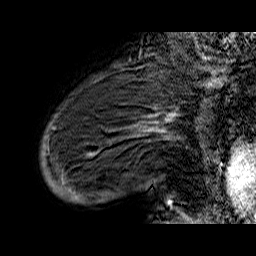
Breast MRI (dynamic contrast-enhanced), one sagittal slice. Slice 9 of 60 in the series (ordered by position). Dynamic contrast-enhanced series, time point 2 of 6 at this slice position (early post-contrast). 1.5 T. TE 6.5 ms, TR 32.9 ms. 4 mm slice thickness. 256 × 256 image matrix. Female patient. From the clinical record (not read from this slice): setting: breast cancer imaged before/during neoadjuvant chemotherapy; receptor status: HR-positive, HER2-negative.
Outlined on this slice (semi-automatic segmentation, software-assisted and operator-edited):
- analysis volume of interest (the breast-tissue region the enhancement analysis was run in; not a lesion): box from (x=41, y=74) to (x=176, y=210) px
- tumour enhancement mask (voxels above the 100 % enhancement threshold inside the analysis volume of interest): (x=155, y=116)–(x=173, y=205)